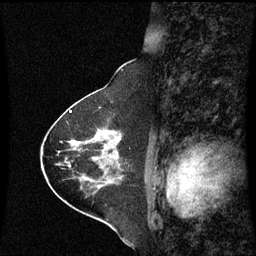
Breast MRI (dynamic contrast-enhanced), one sagittal slice. Position 30 of 60 along the scan axis. Dynamic contrast-enhanced series, image 2 of 3 at this slice position (ordered by acquisition). 1.5 T. TE 4.2 ms, TR 8.9 ms. 2 mm slice thickness. 256 × 256 image matrix. Patient: female, 63 years. Case-level facts recorded for this patient, not image findings: setting: breast cancer imaged before/during neoadjuvant chemotherapy; receptor status: HR-positive, HER2-negative.
Annotated regions visible in this slice (semi-automatic segmentation, software-assisted and operator-edited):
- analysis volume of interest (the breast-tissue region the enhancement analysis was run in; not a lesion): bounding box [x1, y1, x2, y2] px = [88, 130, 123, 163]
- tumour enhancement mask (voxels above the 70 % enhancement threshold inside the analysis volume of interest): [95, 133, 116, 160]